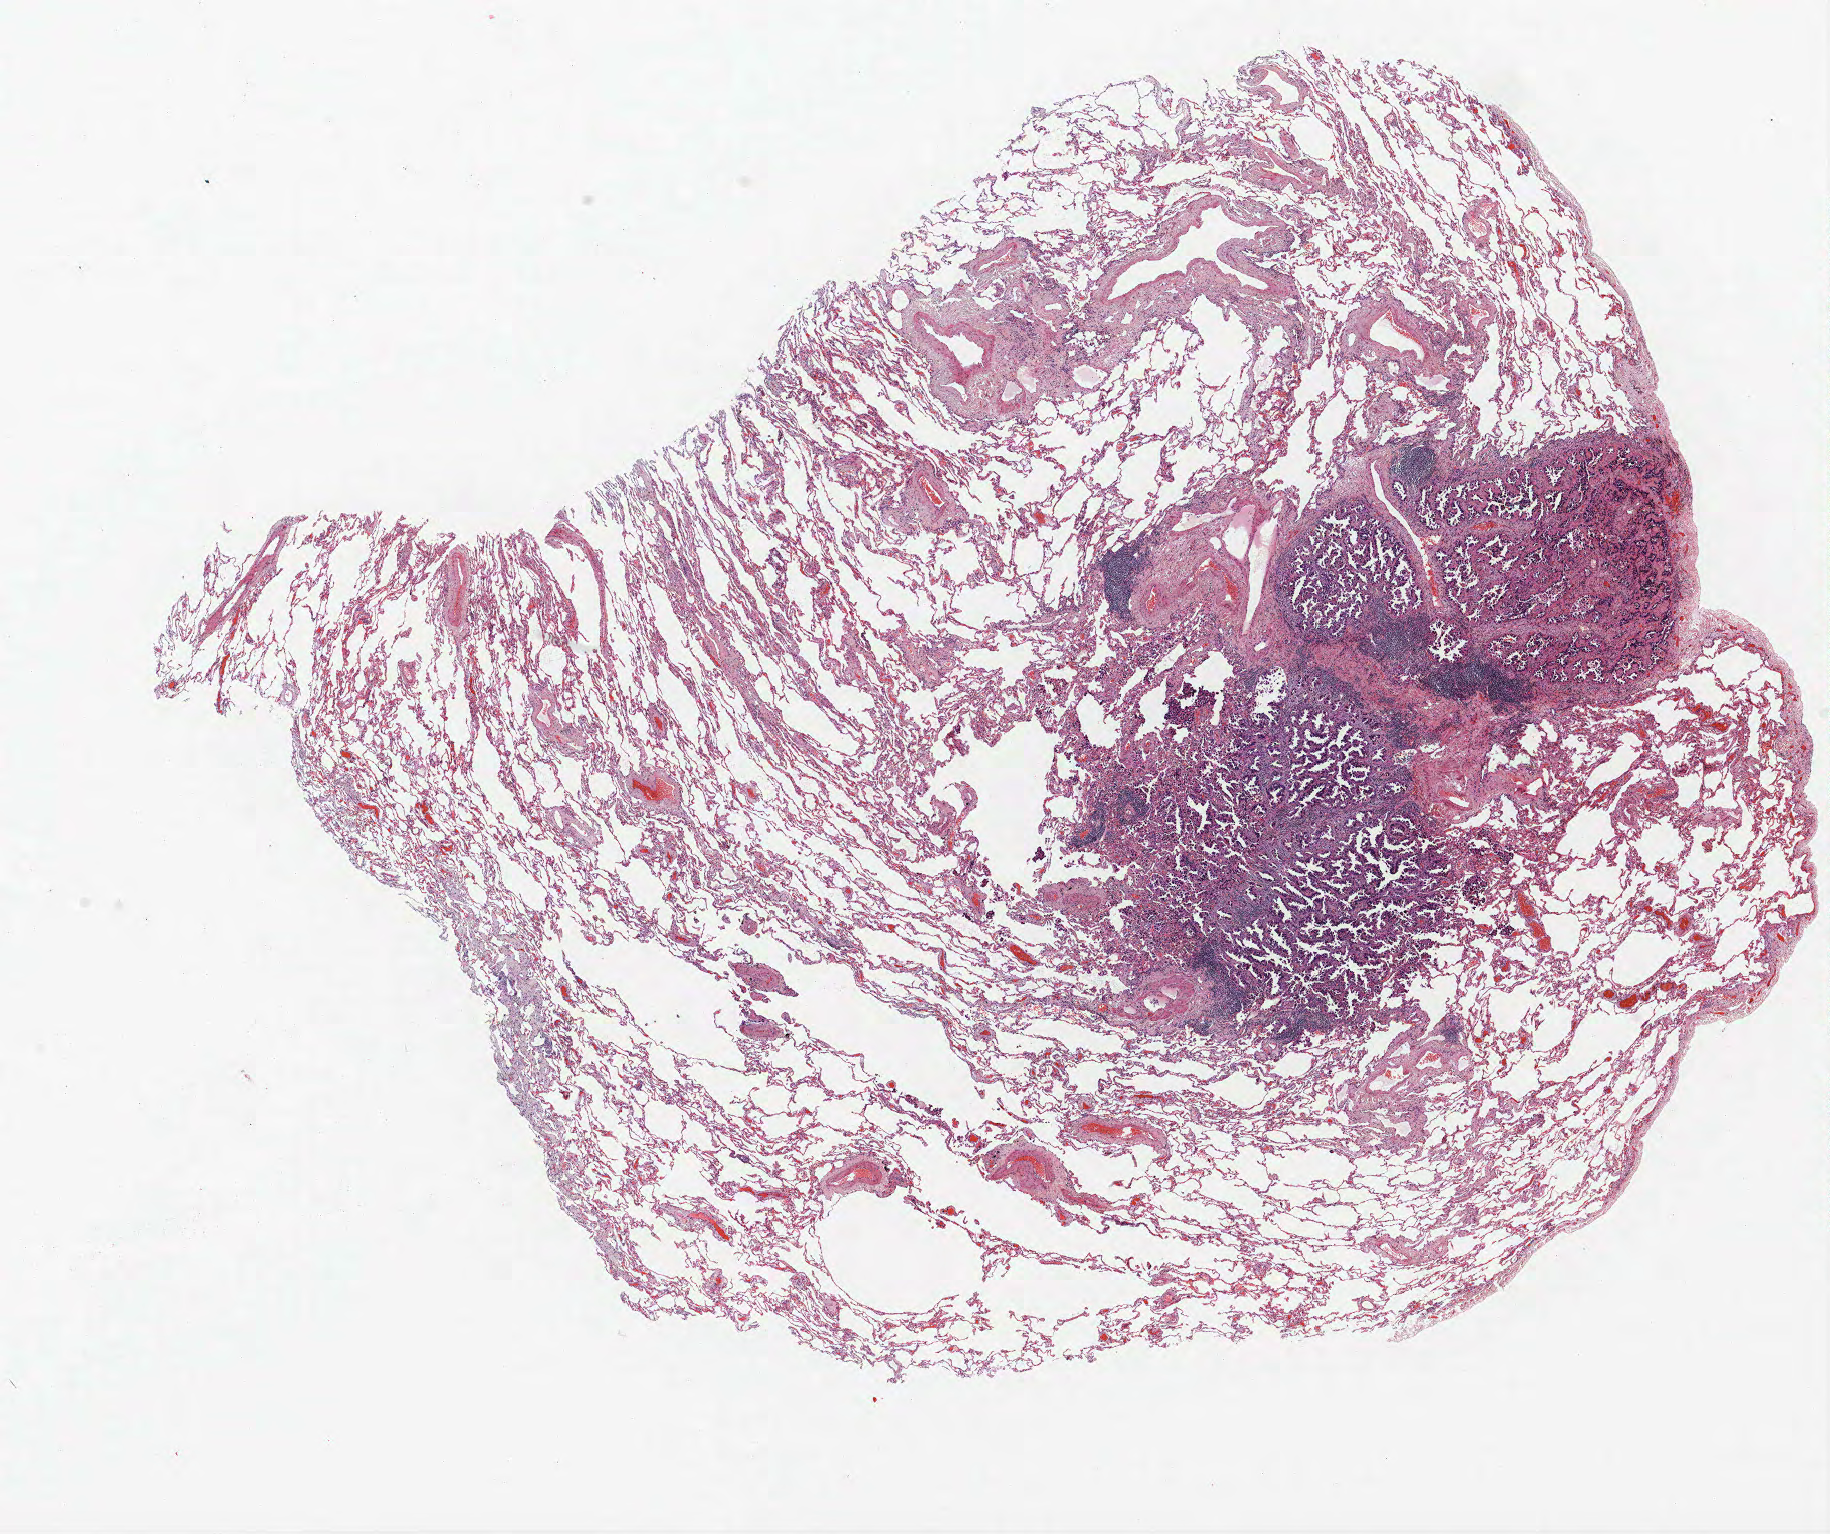
H&E whole-slide image — low-resolution overview of the scanned area, about 14.6 x 12.3 mm; formalin-fixed paraffin-embedded (FFPE) section; lung. Male, age 64 at enrolment.
Participant's lung-cancer diagnosis: Adenocarcinoma, NOS.